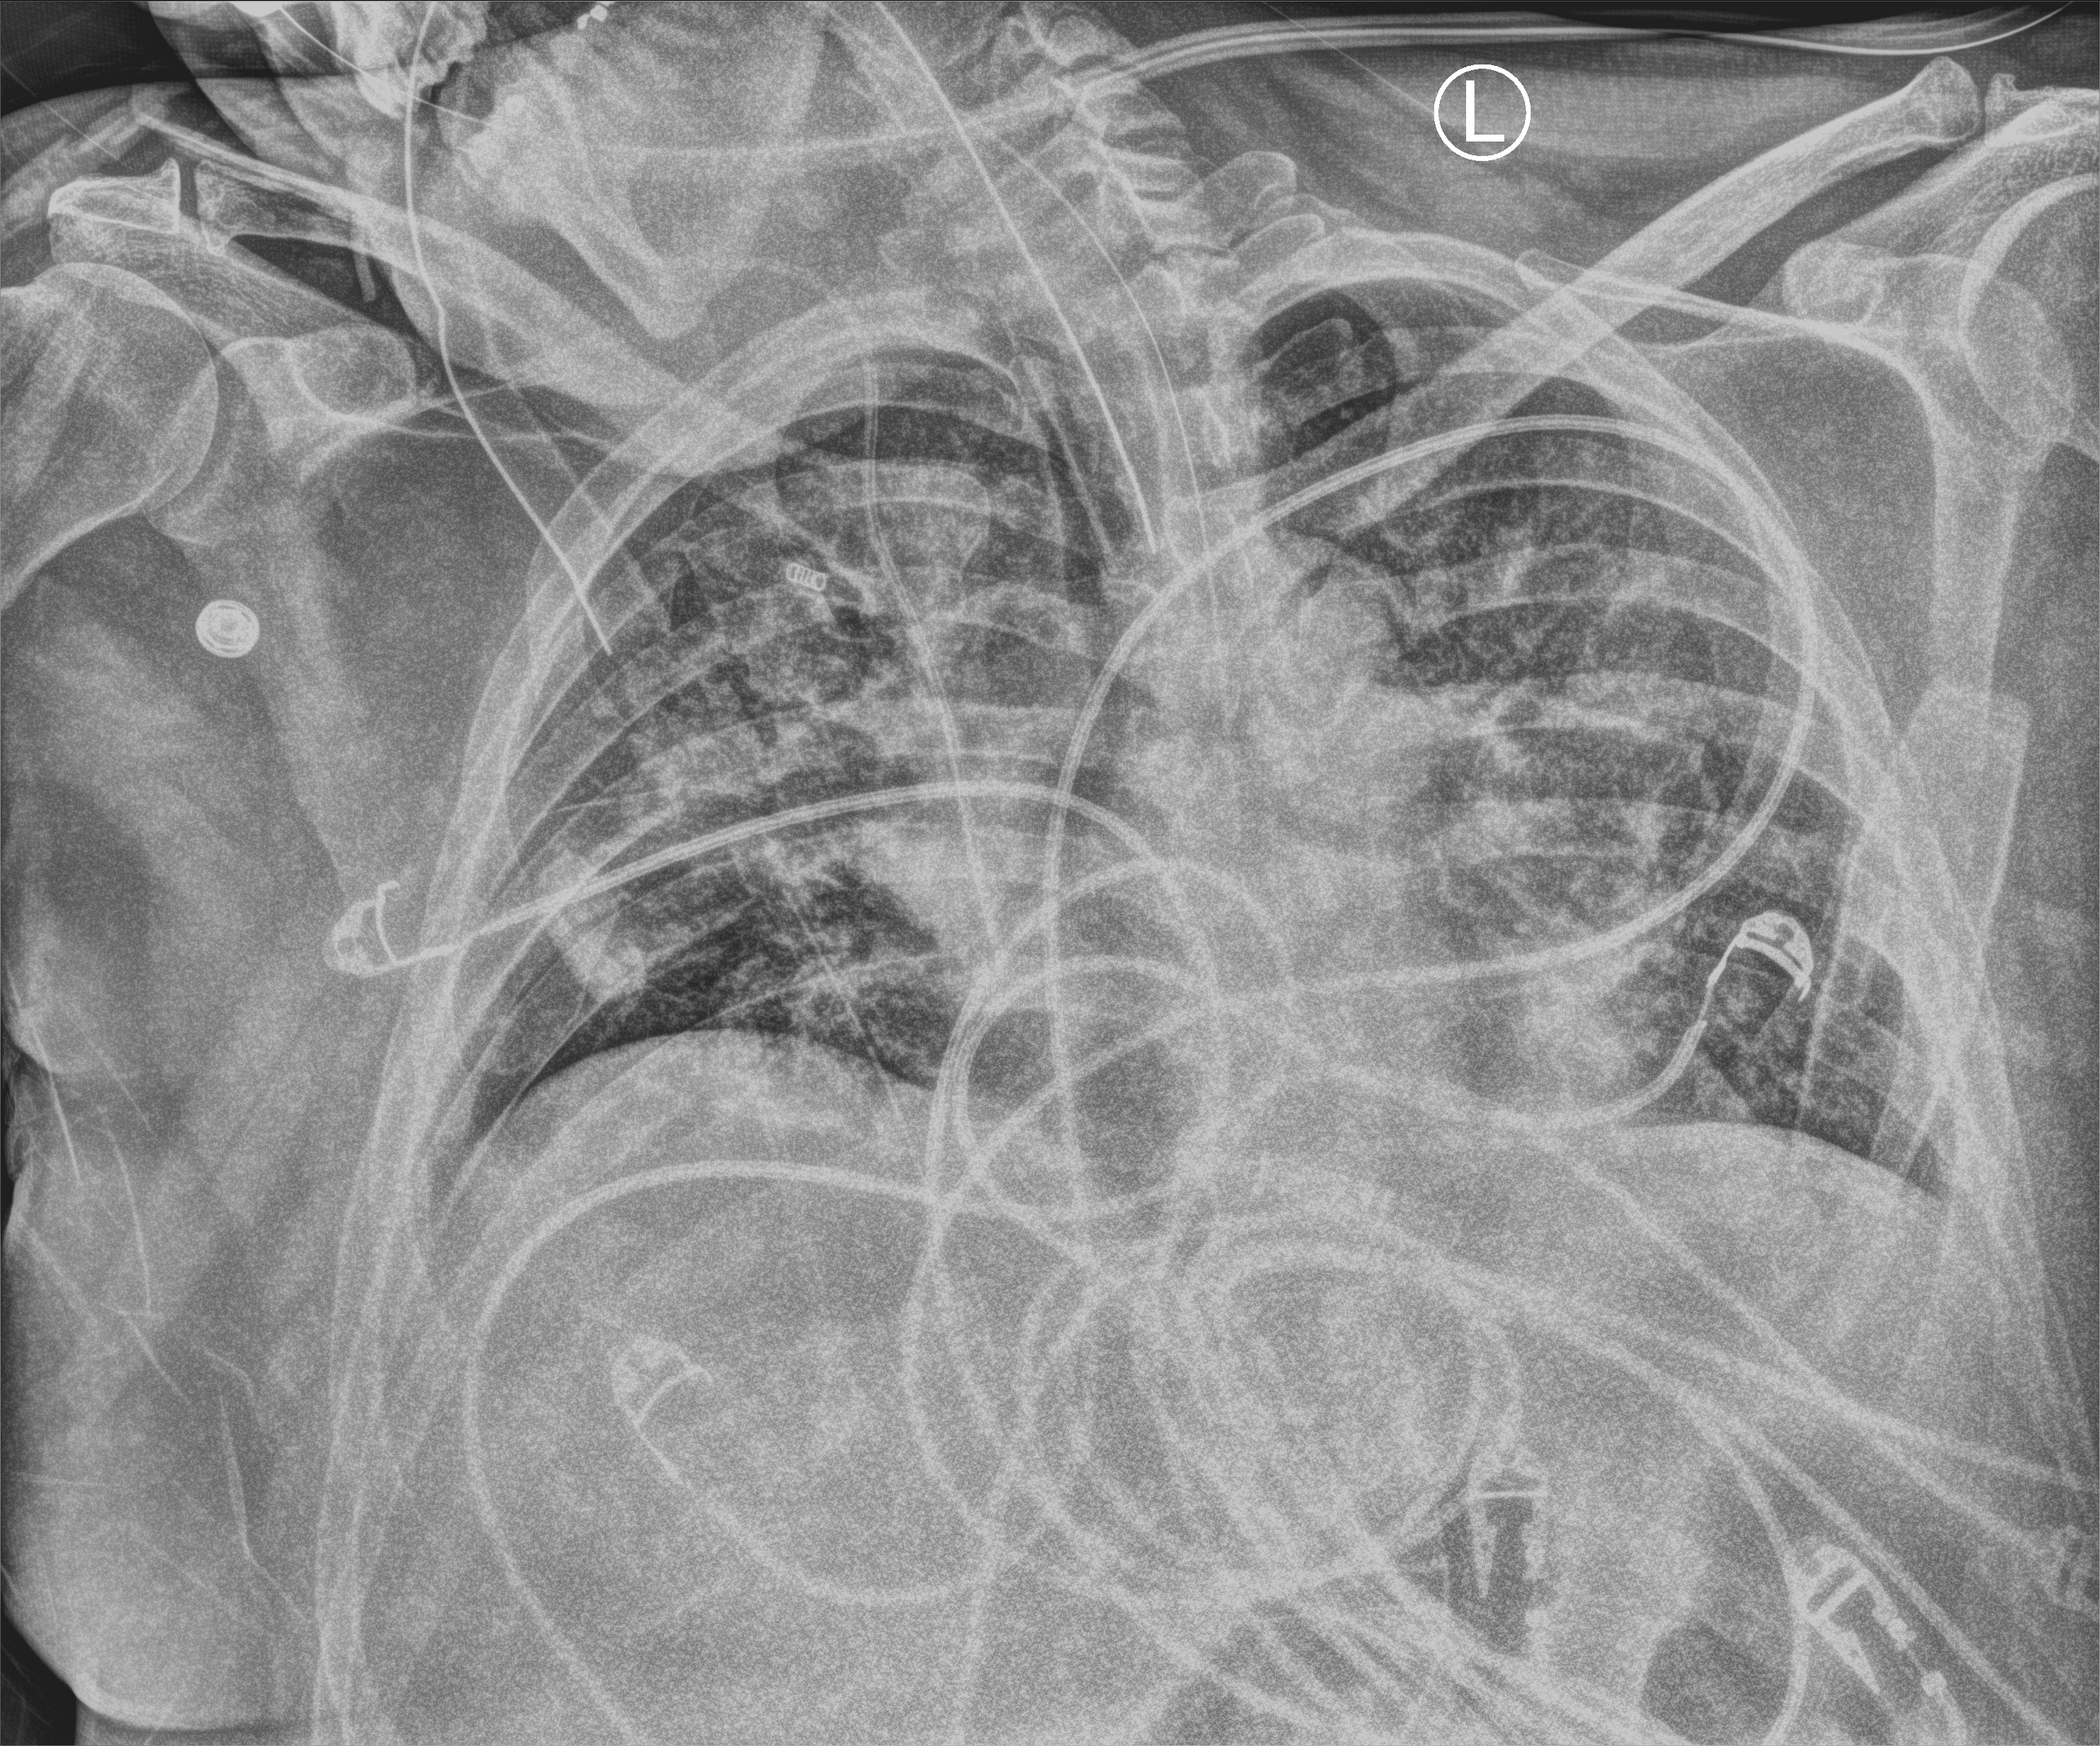
Chest X-ray (portable), anteroposterior (AP) projection. Patient hospitalised with COVID-19; male, aged 18–59 years.
From the hospital-stay record, not from the radiograph (when in the stay this image was taken is not recorded):
- mechanically ventilated during this hospital stay: yes